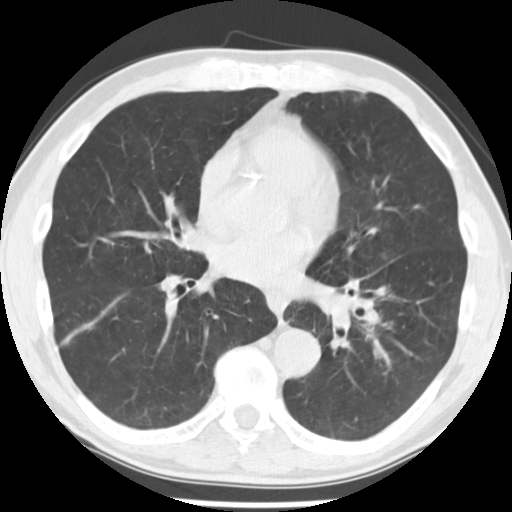
Chest CT (low-dose screening protocol), one axial image. Third annual screen. Lung window (W 1500 / L -600 HU). Male participant, aged 64 years at enrolment. Current smoker at enrolment.
- Lesion marked by an expert reader, box from (x=352, y=318) to (x=390, y=347) px.
- No non-calcified nodule or mass ≥4 mm was recorded by the screening reader at this exam.
- Participant outcome: lung cancer diagnosed 203 days after this screen — adenocarcinoma, NOS, left lower lobe, stage IV (AJCC 6th edition), 44 mm at pathology.